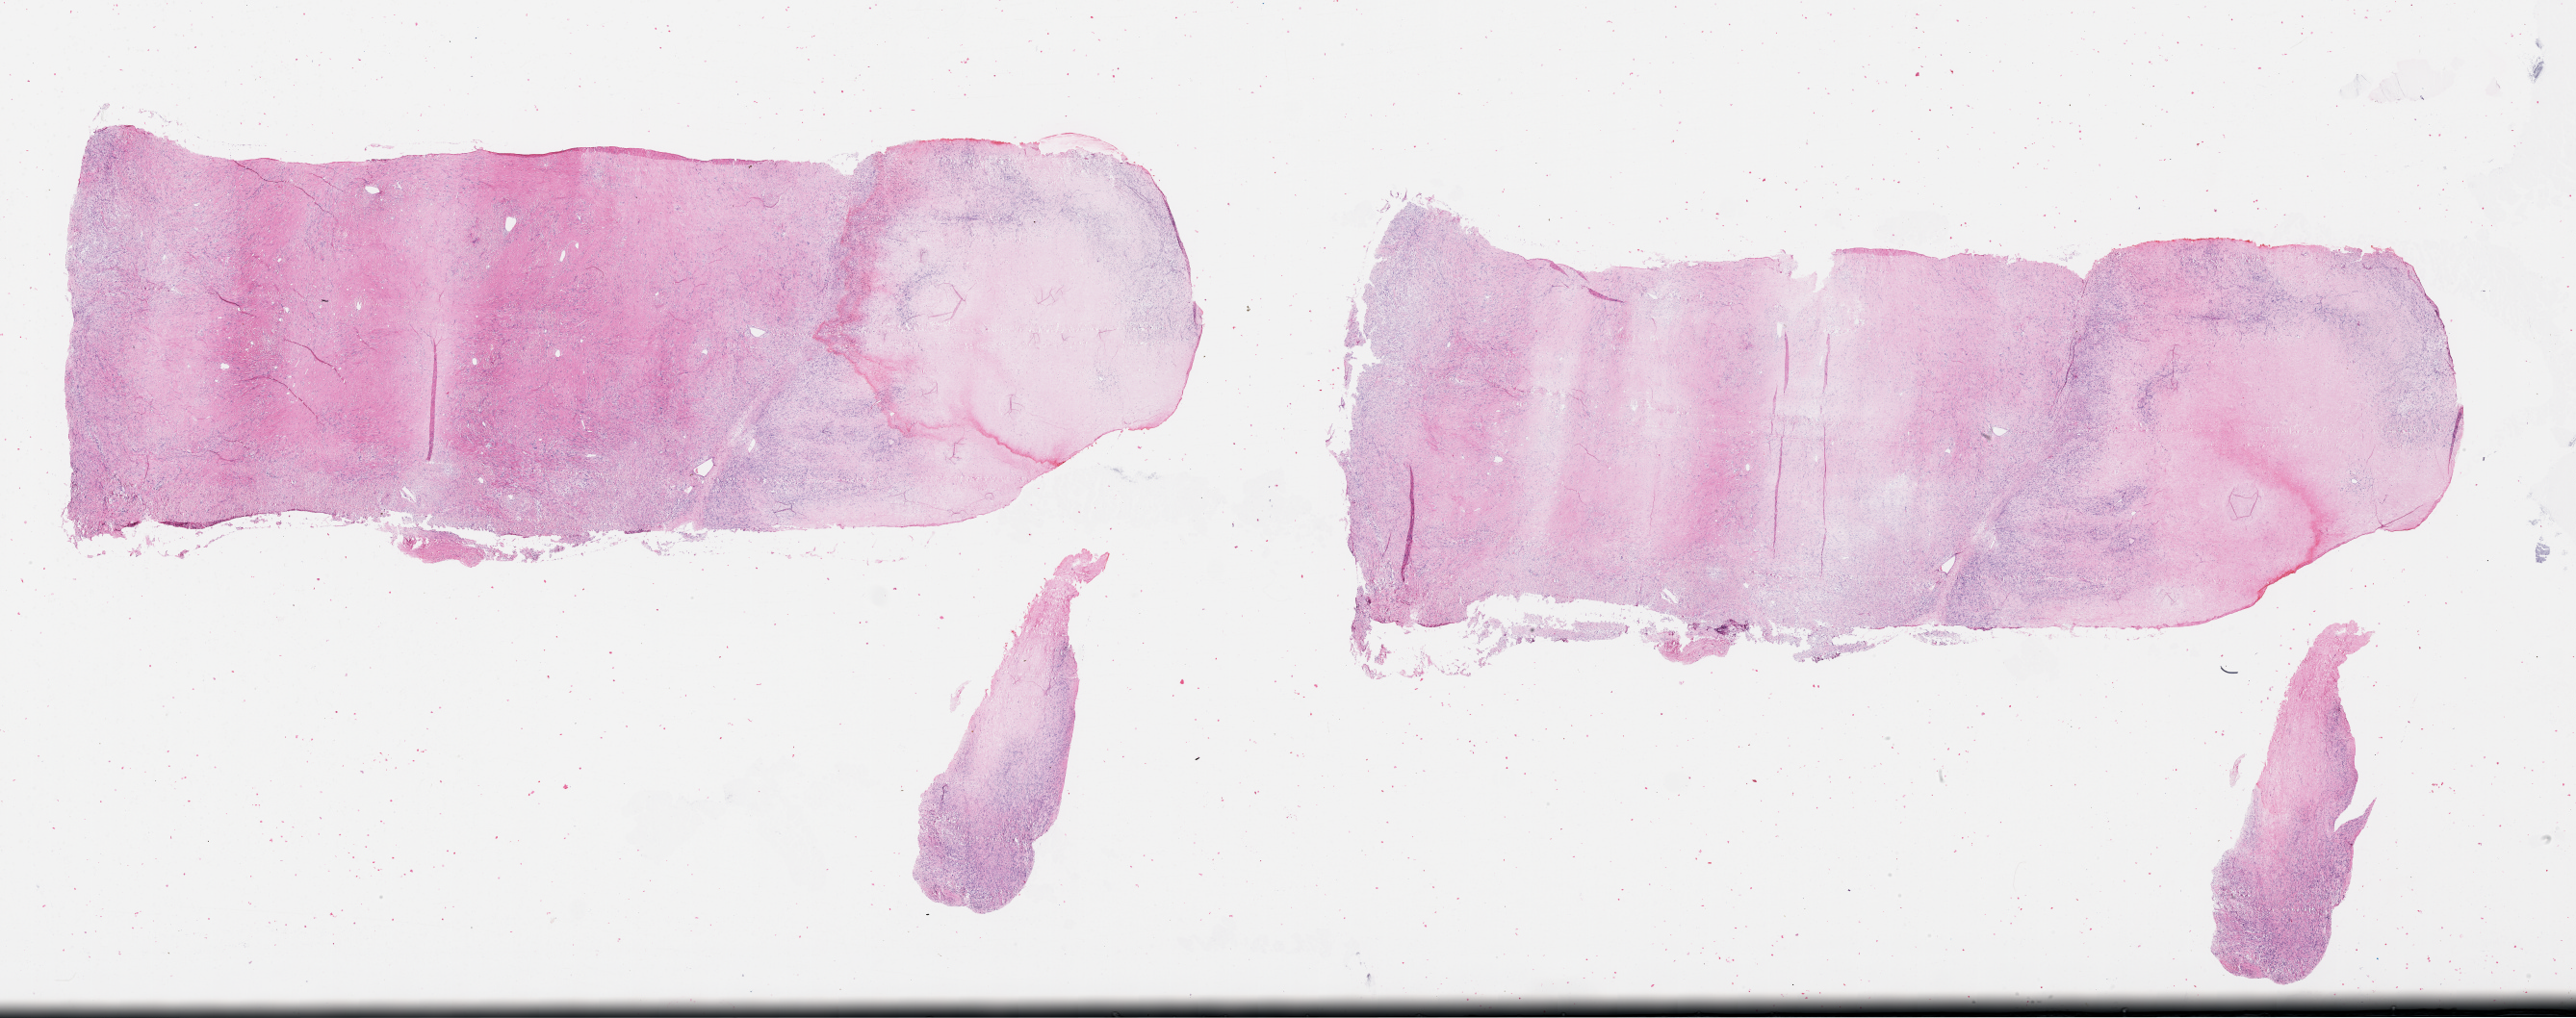
Digitized Hematoxylin and eosin (H&E) stained tissue section (whole slide) — shown as a low-resolution overview of the whole scanned area (about 43.1 x 17.0 mm, acquisition: 20x scan); tumour tissue sample. 62-year-old male patient.
Patient diagnosis (cohort enrolment): sarcoma (site not recorded at cohort level). Primary tumour site (as recorded): chest.